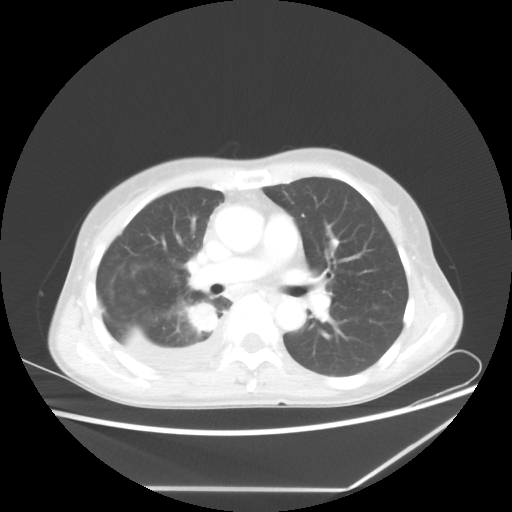
Chest CT, one axial slice. Slice 35 of 60 in the series (ordered by position). Reconstruction kernel STANDARD. Lung window (W 1500 / L -600 HU). 5 mm slice thickness. 512 × 512 image matrix, field of view 364 × 364 mm. Female patient, age 59 years. From the clinical record (not read from this slice): clinical TNM (as recorded): T1c N1 M1.
Structures marked on this image (rectangle marked by the reading radiologist):
- lung tumour (recorded histology: adenocarcinoma): bounding box <186,301,220,333> (left, top, right, bottom; pixels)